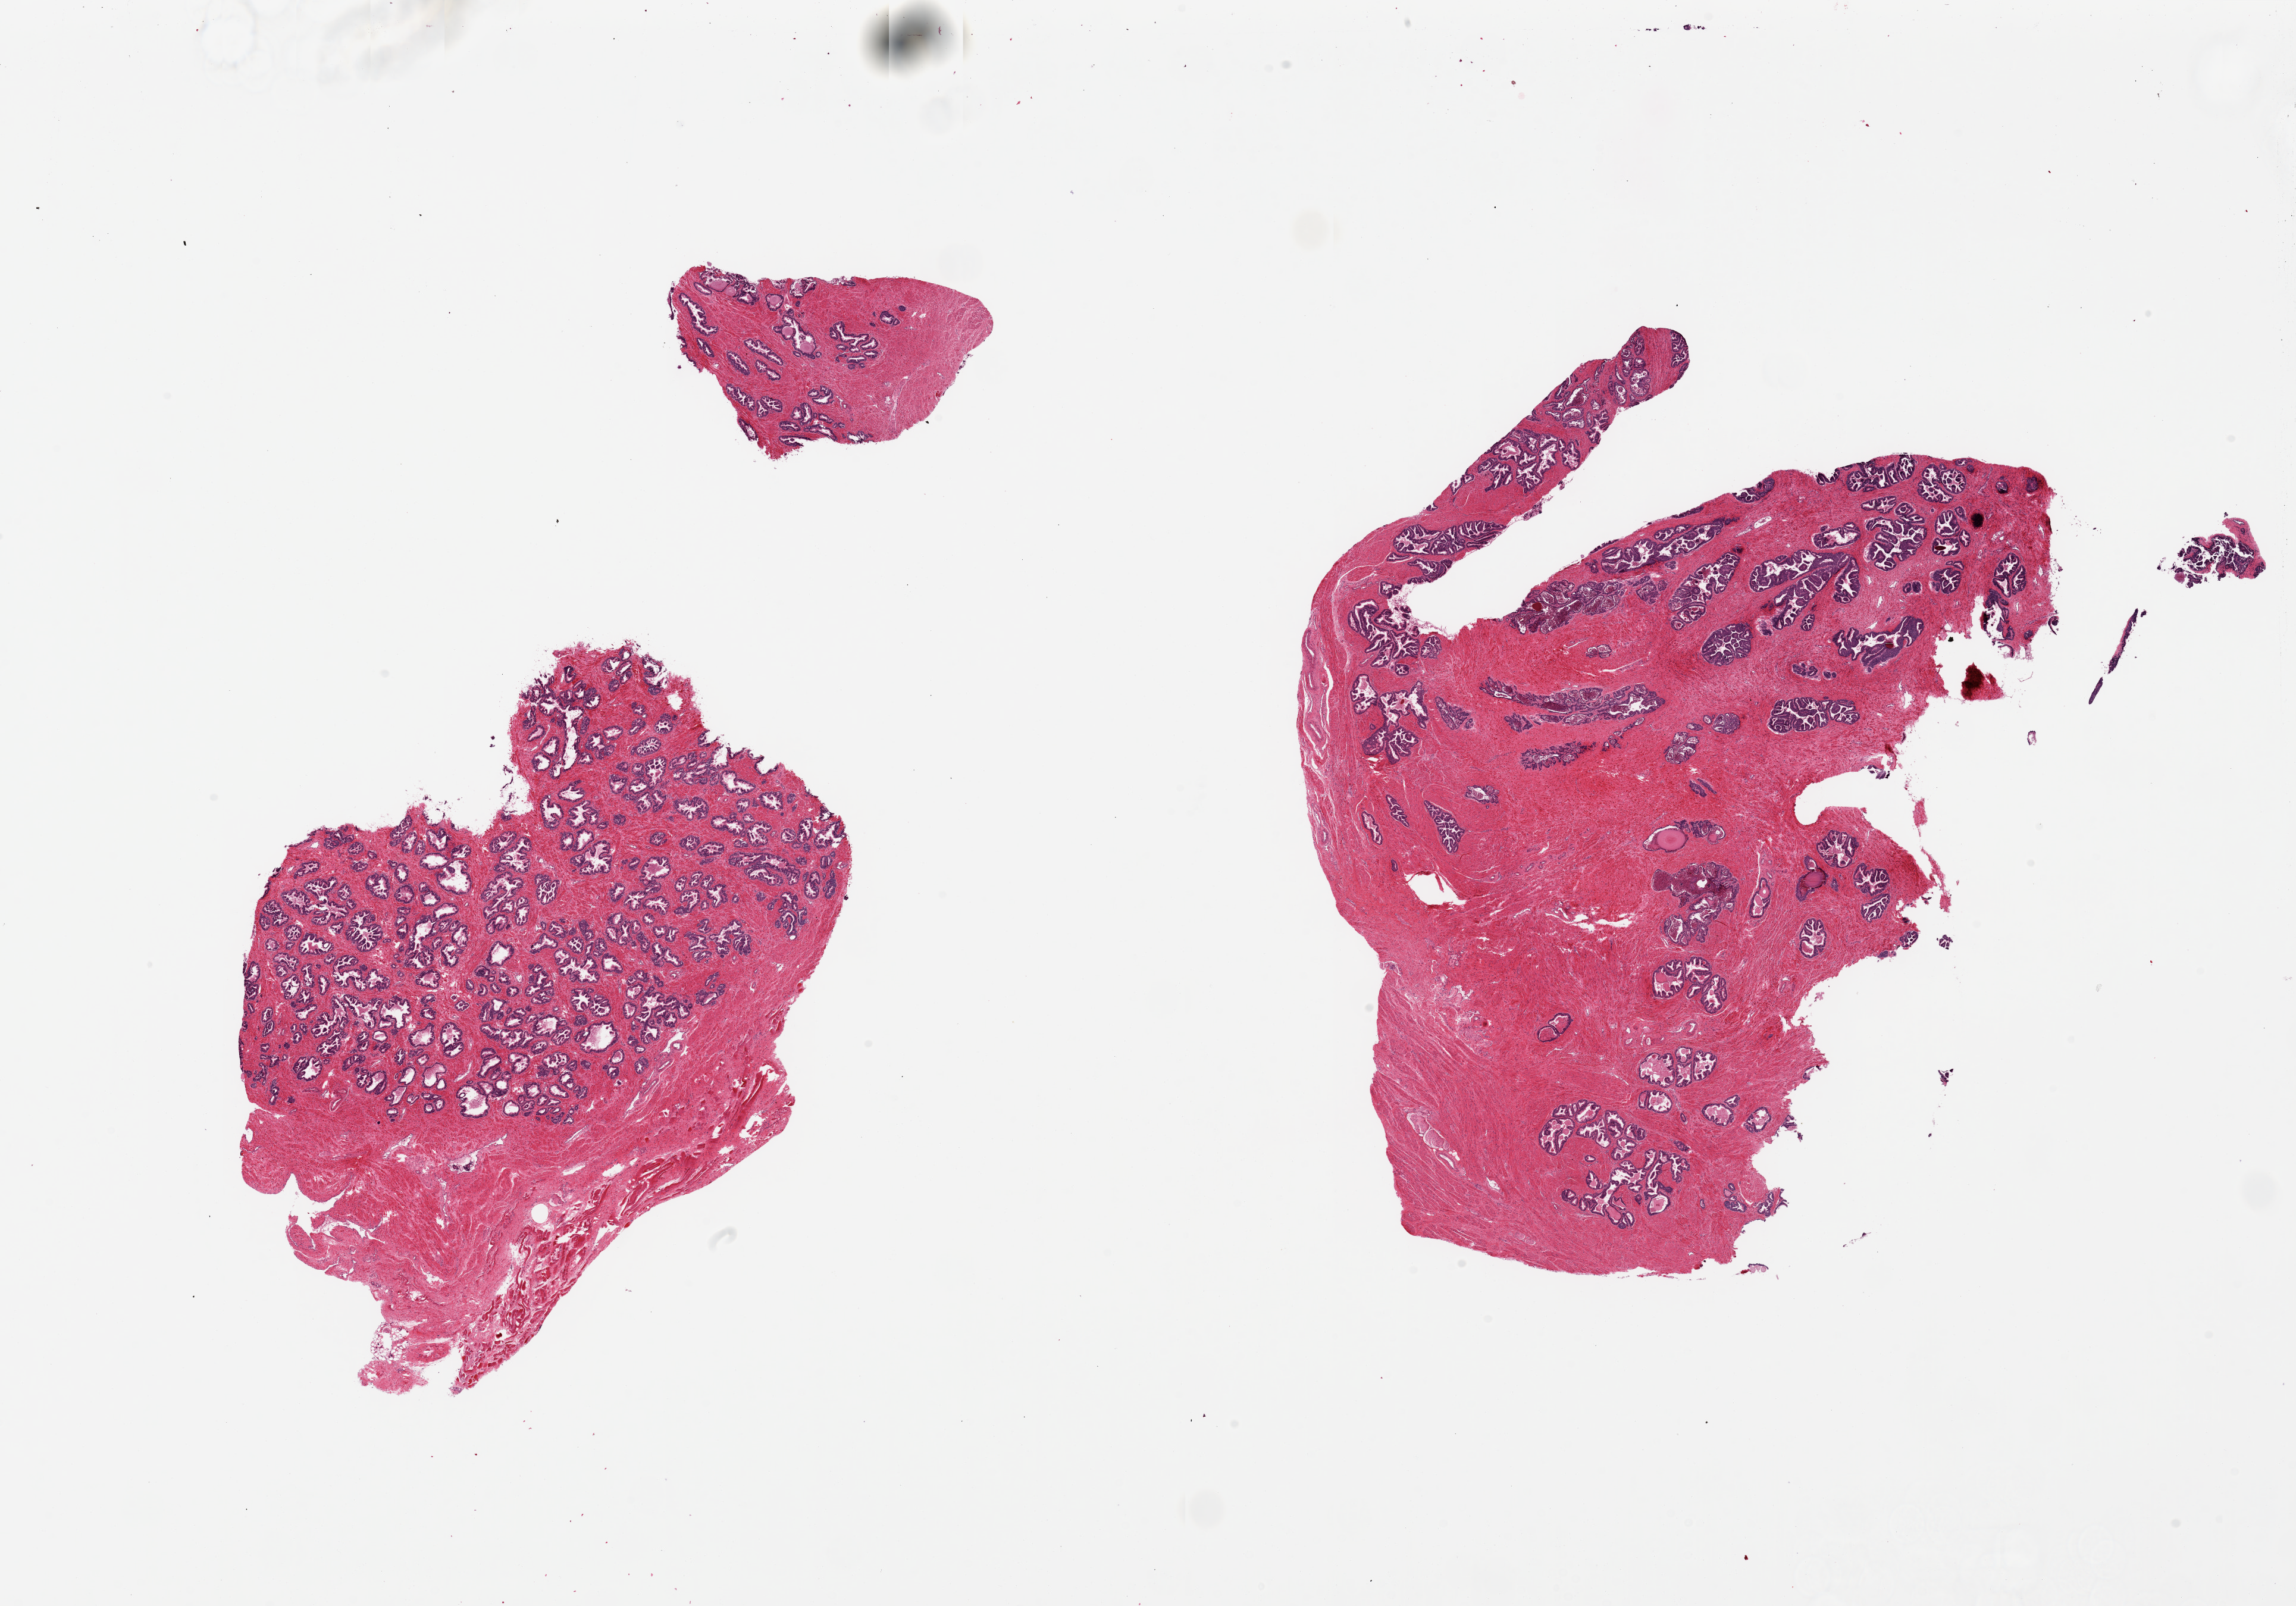
Whole-slide image, hematoxylin and eosin (H&E) stain, brightfield — a low-resolution overview of the entire scanned area, about 30.5 x 21.3 mm (from a 20x scan). PAXgene-fixed, paraffin-embedded tissue. Section of prostate (target tissue). Tissue donor sample. Male donor.
• pathologist's review note for this sample: 2 pieces ~11x7mm. Glandular hyperplasia